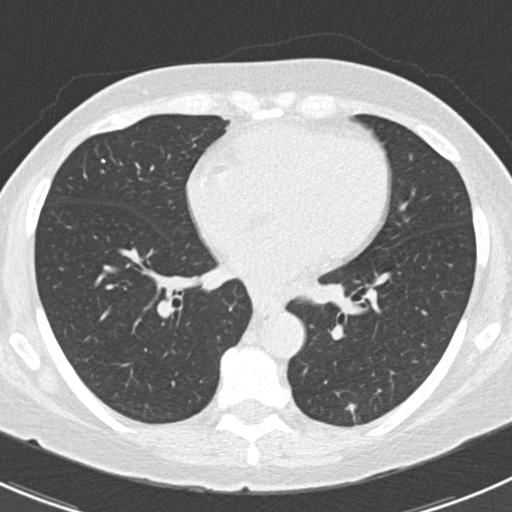
Low-dose screening chest CT, one axial slice. Slice 81 of 166 in the series (ordered by position). Reconstruction kernel B30f. 120 kVp. Lung window (W 1500 / L -600 HU). 2 mm slice thickness. 512 × 512 image matrix.
Annotated regions visible in this slice (expert manual segmentation):
- lesion 1 (tumor, lower lobe of left lung): box from (x=346, y=403) to (x=356, y=415) px